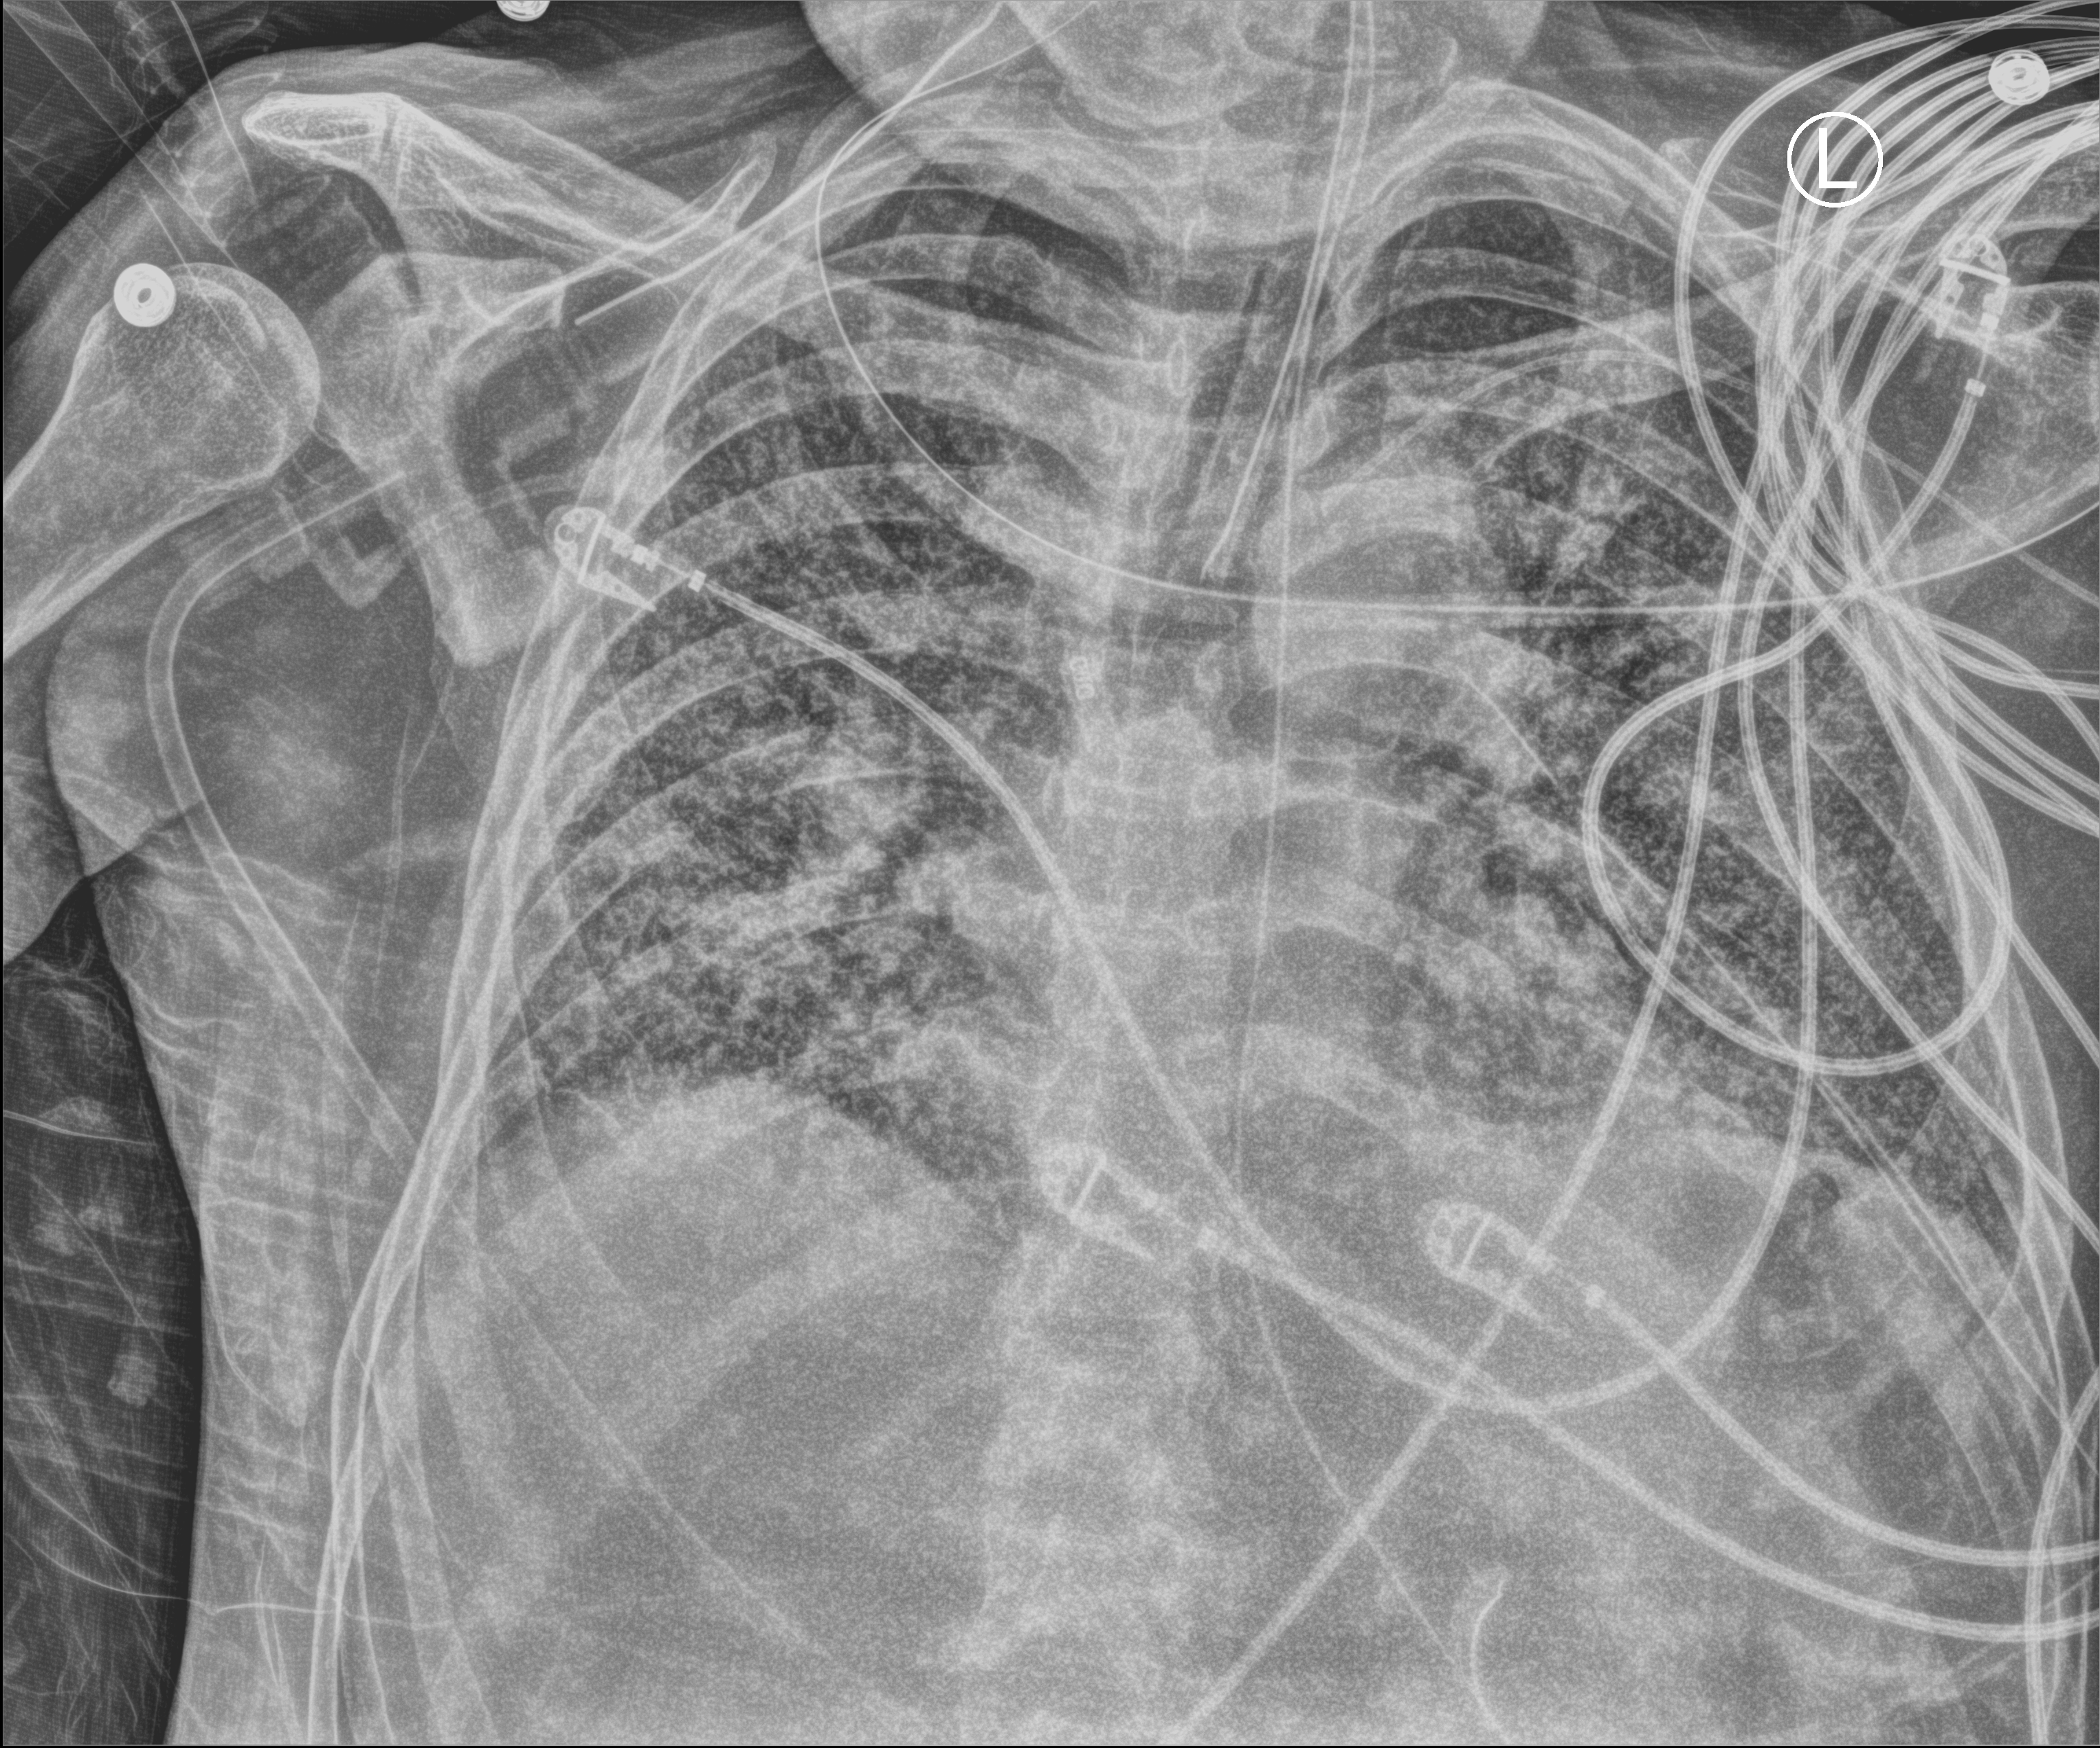
Portable chest radiograph; anteroposterior (AP) projection. Patient hospitalised with COVID-19; male, aged 60–74 years.
From the hospital-stay record, not from the radiograph (when in the stay this image was taken is not recorded): mechanically ventilated during this hospital stay: yes; admitted to intensive care during this hospital stay: yes.